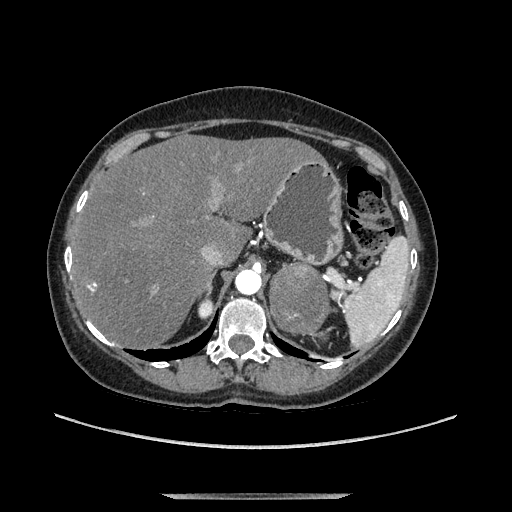
Contrast-enhanced abdominal CT, one axial slice; position 95 of 169 along the scan axis; soft-tissue window (W 400 / L 40 HU); 1.25 mm slice thickness; 512 × 512 image matrix. Female patient. From the clinical record (not read from this slice): diagnosis: adrenocortical carcinoma; tumour side: left adrenal; tumour size at pathology: 9 cm; Ki-67 index: 2 %; stage (as recorded): 3.
Annotated regions visible in this slice (semi-automatically segmented with operator editing):
- mass: bounding box [x1, y1, x2, y2] px = [271, 264, 328, 332]